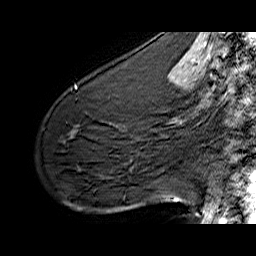
Breast MRI (dynamic contrast-enhanced), one sagittal slice. Slice 38 of 60 in the series (ordered by position). Dynamic contrast-enhanced series, time point 2 of 6 at this slice position (early post-contrast). 1.5 T. TE 6.4 ms, TR 32.9 ms. 256 × 256 image matrix. Female patient. From the clinical record (not read from this slice): setting: breast cancer imaged before/during neoadjuvant chemotherapy; receptor status: HER2-positive.
Structures marked on this image (semi-automatic segmentation, software-assisted and operator-edited):
- analysis volume of interest (the breast-tissue region the enhancement analysis was run in; not a lesion): bounding box (x1, y1, x2, y2) in pixels: (61, 77, 141, 142)
- tumour enhancement mask (voxels above the 100 % enhancement threshold inside the analysis volume of interest): (75, 86, 77, 88)